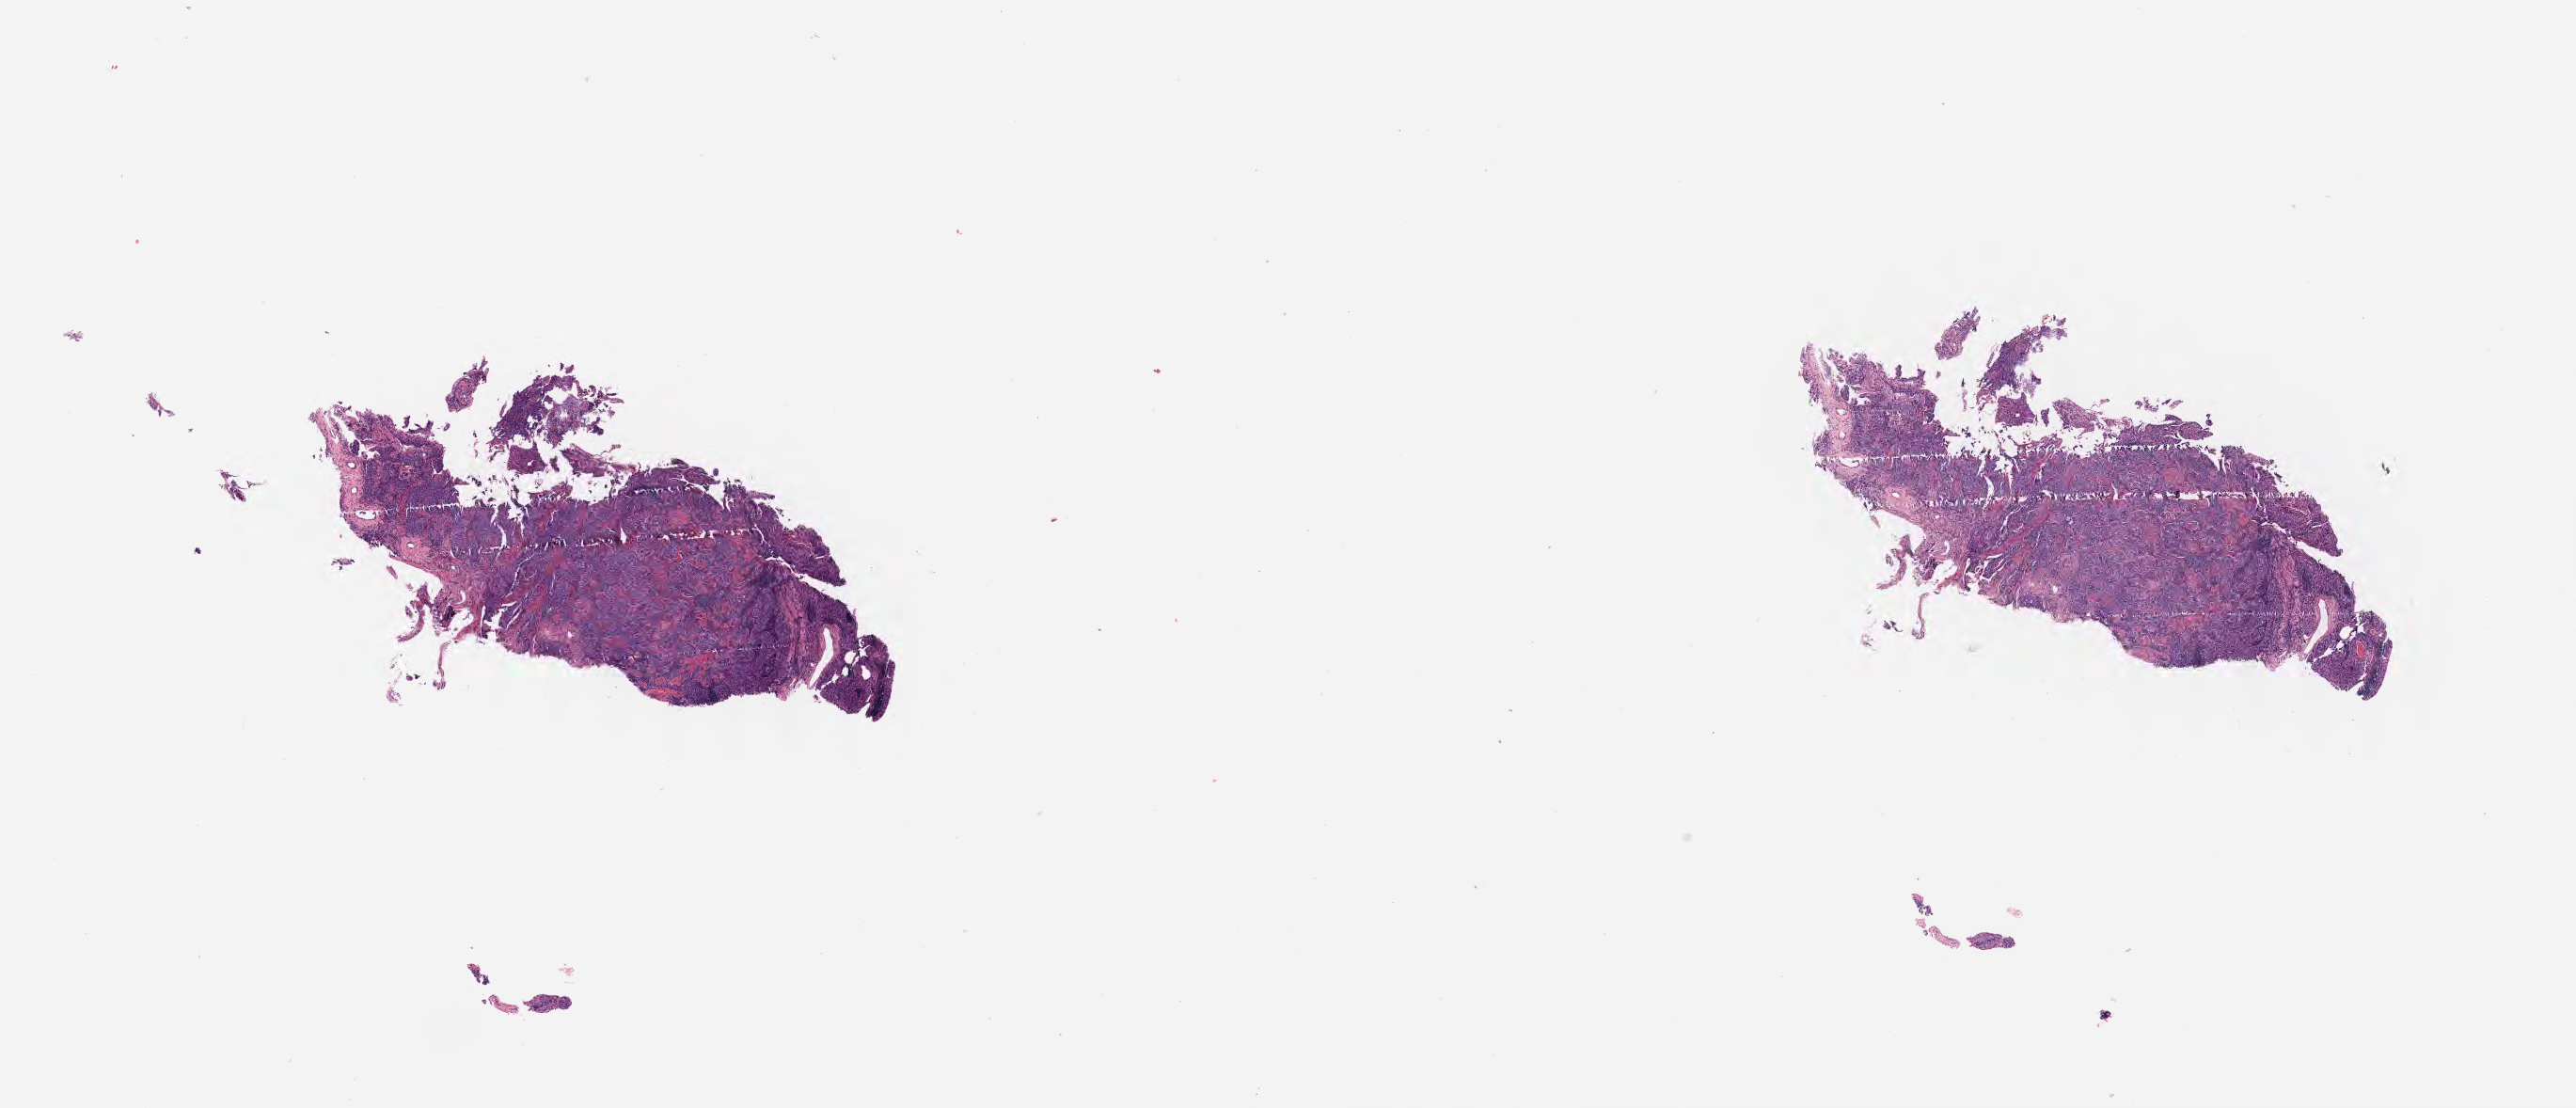
Whole-slide image, hematoxylin and eosin (H&E) stain, low-resolution overview of the scanned area, about 22.1 x 9.5 mm. Tumor tissue. Anatomic site: cervix. Female patient, 58 years old.
- histologic diagnosis: Squamous cell carcinoma, large cell, nonkeratinizing, NOS